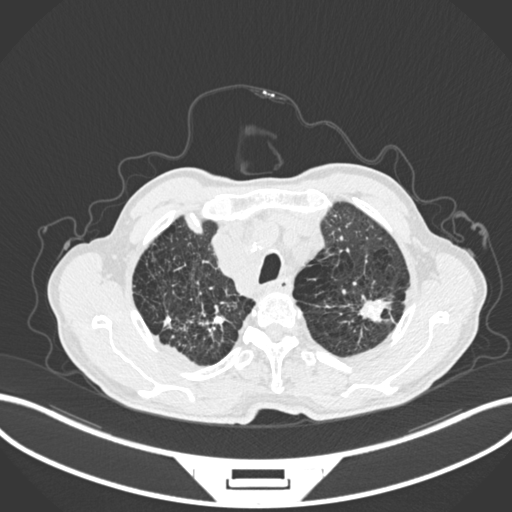
Chest CT, one axial slice; position 232 of 287 along the scan axis; reconstruction kernel B30f; 120 kVp; lung window (W 1500 / L -600 HU); 1 mm slice thickness; 512 × 512 image matrix, field of view 400 × 400 mm. Male patient, age 74 years. From the clinical record (not read from this slice): clinical TNM (as recorded): T2a N1 M0.
Outlined on this slice (rectangle marked by the reading radiologist):
- lung tumour (recorded histology: adenocarcinoma): box from (x=355, y=295) to (x=394, y=325) px